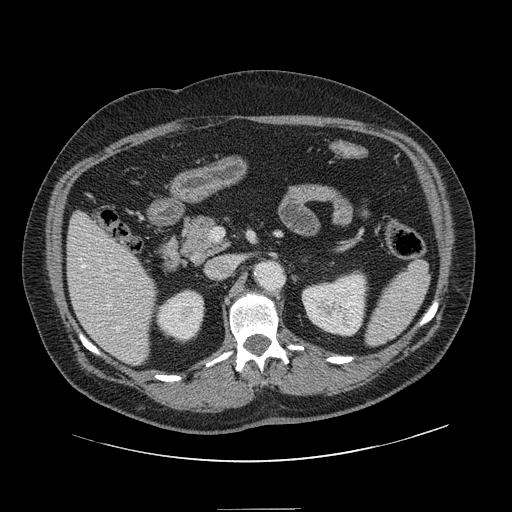
Contrast-enhanced abdominal CT, one axial slice. 120 kVp. Intravenous contrast given. Soft-tissue window (W 400 / L 40 HU). 512 × 512 image matrix, field of view 451 × 451 mm. Male patient, age 61 years. Case-level facts recorded for this patient, not image findings: diagnosis: colorectal cancer liver metastases, imaged before liver resection; multiple liver metastases: yes; largest metastasis: 2.6 cm.
Outlined on this slice (outlined manually by an expert reader):
- hepatic veins: box from (x=82, y=260) to (x=119, y=331) px
- liver: (x=68, y=213)–(x=157, y=364)
- planned liver remnant (the part of the liver to remain after resection): (x=69, y=213)–(x=157, y=363)